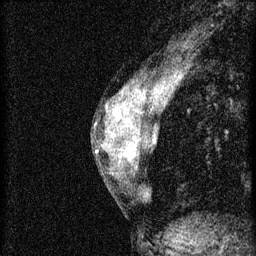
Breast MRI (dynamic contrast-enhanced), one sagittal slice; position 24 of 46 along the scan axis; 3 images stored at this slice position (order not interpretable as contrast timing); 1.5 T; TE 4.2 ms, TR 8.2 ms; 256 × 256 image matrix. Patient: female, 44 years.
Annotated regions visible in this slice (semi-automatically segmented with operator editing):
- analysis volume of interest (the breast-tissue region the enhancement analysis was run in; not a lesion): bounding box <110,128,156,181> (left, top, right, bottom; pixels)
- tumour enhancement mask (voxels above the 70 % enhancement threshold inside the analysis volume of interest): <122,136,156,163>